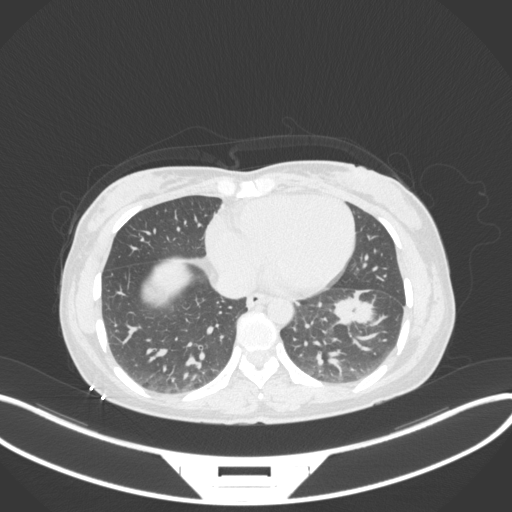
Chest CT, one axial slice. Position 122 of 361 along the scan axis. Reconstruction kernel B31f. Lung window (W 1500 / L -600 HU). 512 × 512 image matrix, field of view 400 × 400 mm. Female patient, age 41 years. Case-level facts recorded for this patient, not image findings: clinical TNM (as recorded): T2a N3 M1b.
Annotated regions visible in this slice (rectangle marked by the reading radiologist):
- lung tumour (recorded histology: adenocarcinoma): box from (x=335, y=291) to (x=377, y=327) px